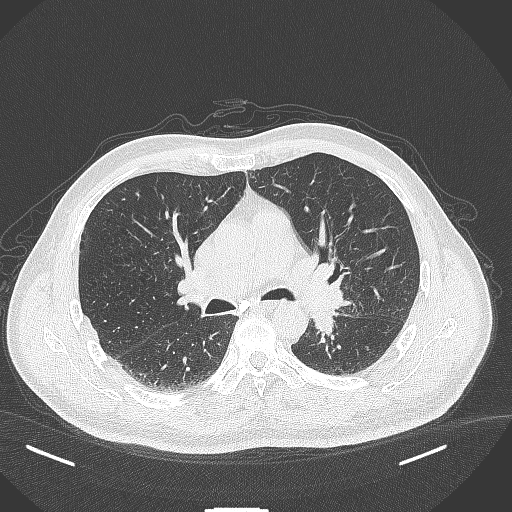
Chest CT, one axial slice. Slice 248 of 429 in the series (ordered by position). Reconstruction kernel B70f. 120 kVp. Lung window (W 1500 / L -600 HU). 1 mm slice thickness. 512 × 512 image matrix. Patient: male, 55 years. Case-level facts recorded for this patient, not image findings: clinical TNM (as recorded): T3 N0 M1c; histopathological grade: G3.
Annotated regions visible in this slice (bounding box drawn by a radiologist):
- lung tumour (recorded histology: adenocarcinoma): bounding box [x1, y1, x2, y2] px = [309, 303, 339, 338]